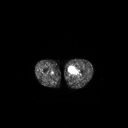
FDG PET of an extremity soft-tissue mass (from a PET/CT study), one axial slice; position 227 of 267 along the scan axis; 3.27 mm slice thickness; 128 × 128 image matrix, field of view 700 × 700 mm. Male patient, age 63 years. Case-level facts recorded for this patient, not image findings: histological type: pleiomorphic liposarcoma; grade: high; site of the primary tumour: left thigh.
Outlined on this slice (expert contour drawn on MRI and transferred to this co-registered scan by the dataset authors):
- gross tumour volume including surrounding oedema: box from (x=68, y=65) to (x=80, y=75) px
- gross tumour volume (mass): (x=68, y=65)–(x=75, y=73)